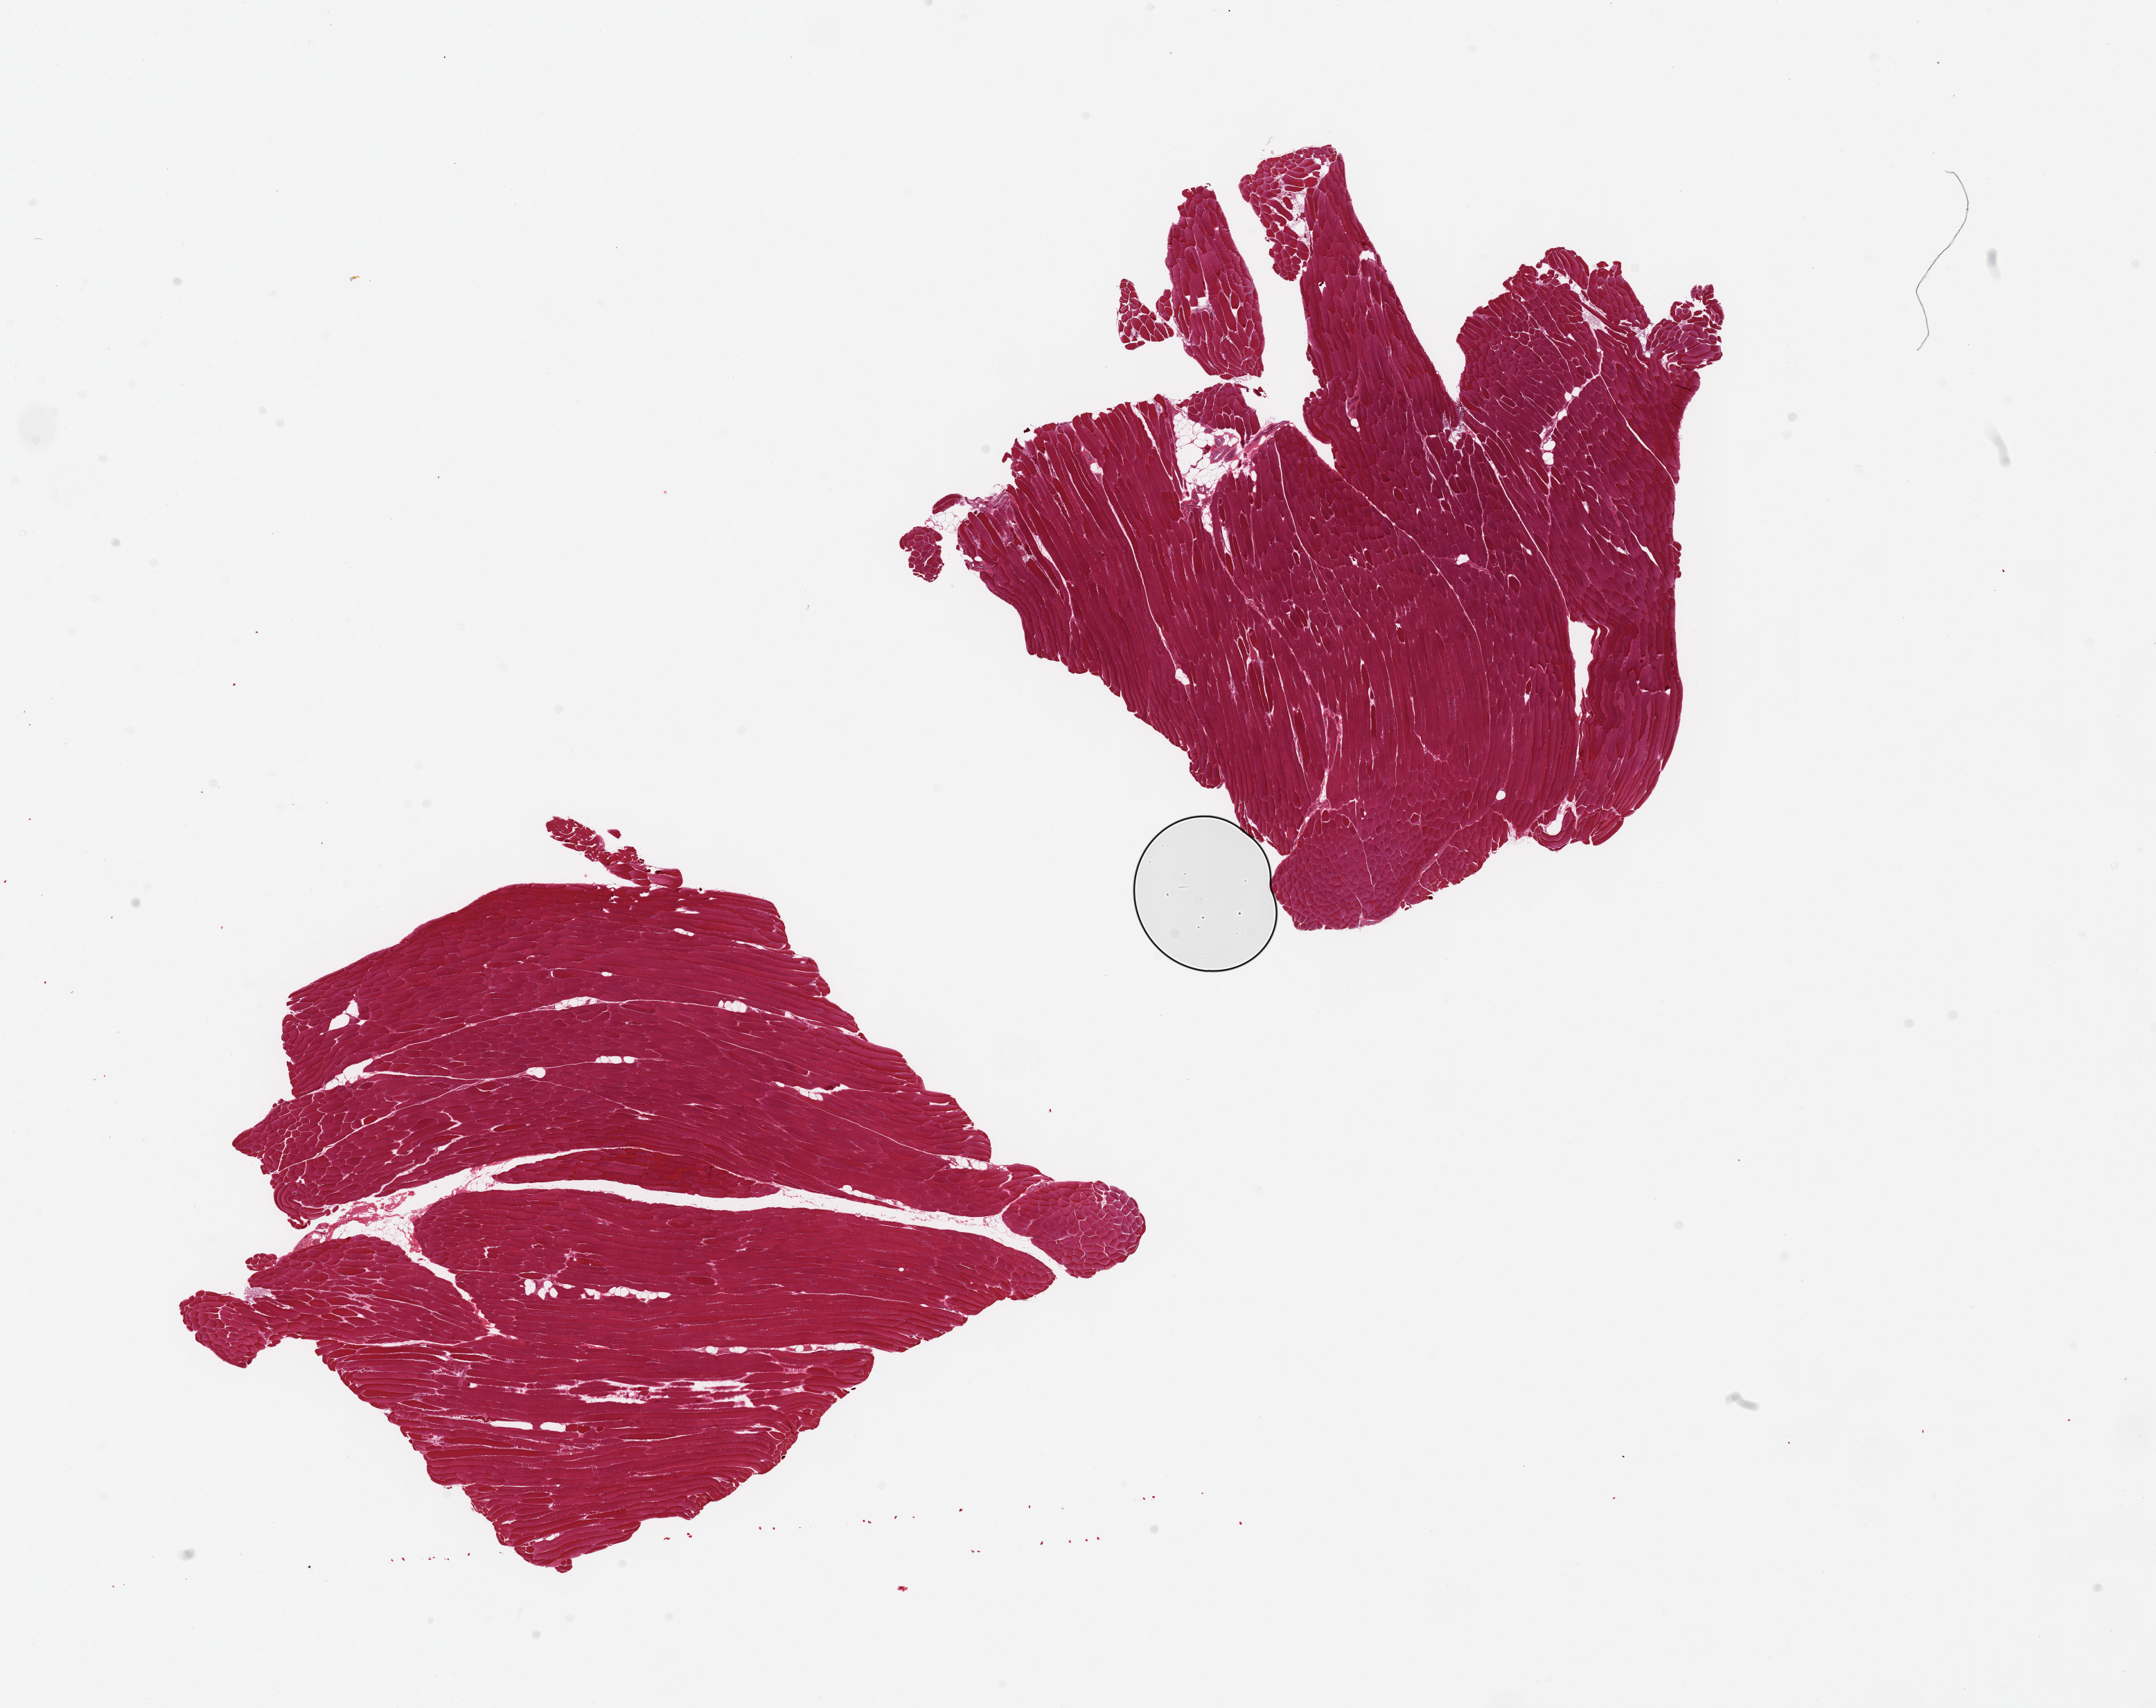
Whole-slide image, H&E stain, shown as a low-resolution overview of the whole scanned area (about 24.6 x 19.5 mm), PAXgene-fixed paraffin-embedded (PFPE) section, target tissue: skeletal muscle, tissue donor sample. Donor: male.
* pathologist's review note for this sample: 2 pieces; minimal internal fat